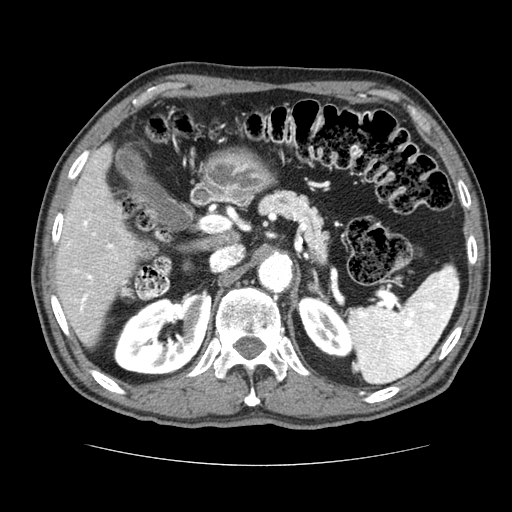
Contrast-enhanced abdominal CT (liver protocol), one axial slice. Slice 41 of 79 in the series (ordered by position). Soft-tissue window (W 400 / L 40 HU). 512 × 512 image matrix, field of view 360 × 360 mm. Case-level facts recorded for this patient, not image findings: diagnosis: hepatocellular carcinoma (patient treated with transarterial chemoembolisation; whether this scan precedes or follows treatment is not stated here); TNM stage (as recorded): Stage-I.
Annotated regions visible in this slice (semi-automatic segmentation, software-assisted and operator-edited):
- liver parenchyma outside the tumour (the mass and vessels are separate outlines, so this box may not span the whole liver): box from (x=54, y=144) to (x=140, y=347) px
- liver vessels: (x=66, y=162)–(x=125, y=314)